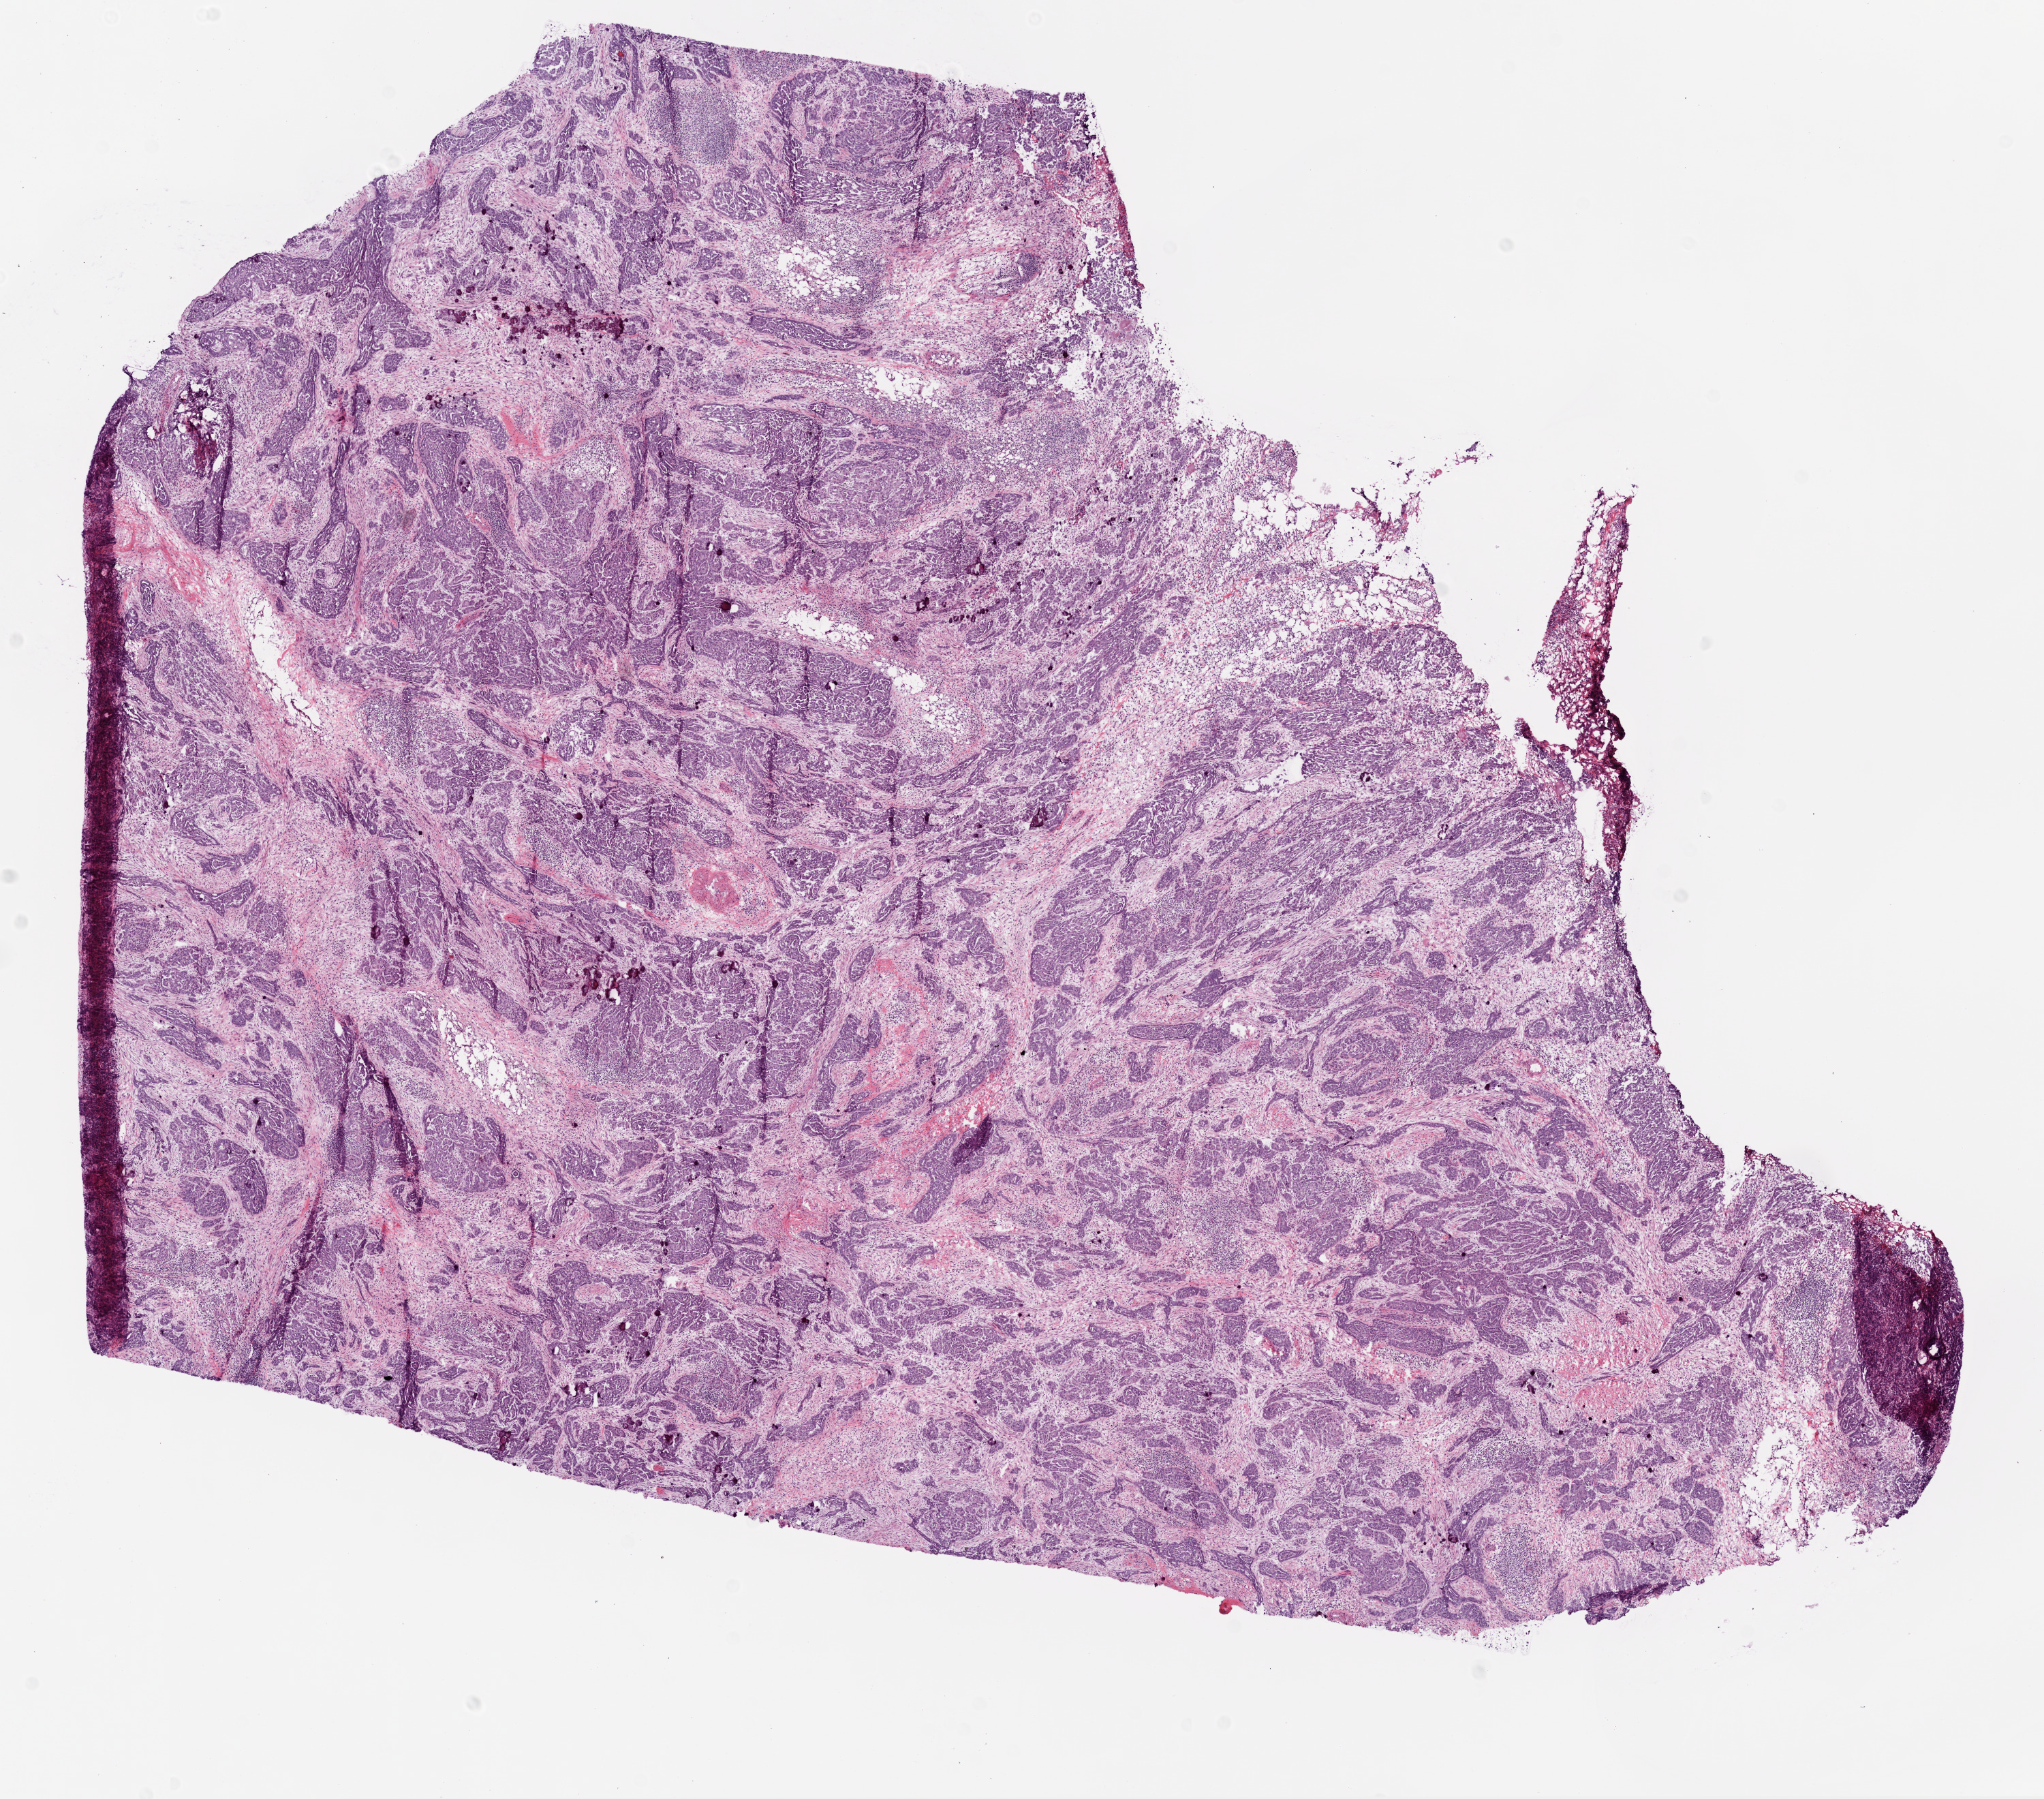
Whole-slide histology image, H&E-stained — a low-resolution overview of the entire scanned area, about 12.0 x 10.6 mm, frozen section from the top of the tissue portion, sample: primary tumour, ovary. Female patient; age at initial diagnosis 52 years. Slide review estimates, as recorded: tumour cells 90%, tumour nuclei 90%.
Pathologic diagnosis: Serous cystadenocarcinoma, NOS.